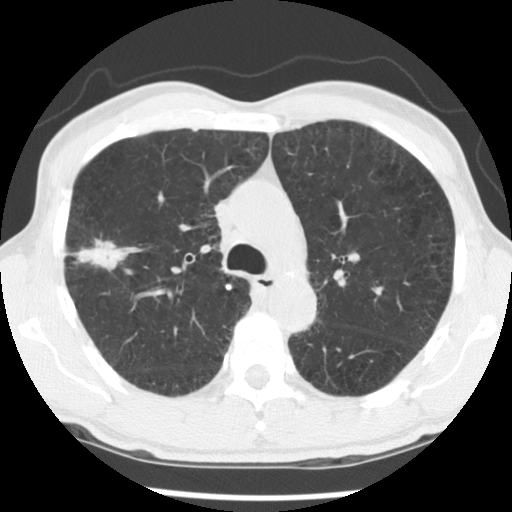
Chest CT (low-dose screening protocol), one axial image; second screening round (one year after baseline); lung window (W 1500 / L -600 HU); standard (soft-tissue) reconstruction kernel (STANDARD); 140 kVp; 512 × 512 image matrix, field of view 320 × 320 mm. Male participant, aged 56 years at enrolment. Current smoker at enrolment.
Lesion marked by an expert reader, box from (x=53, y=231) to (x=139, y=293) px. Reader record for this screening exam (exam-level; its link to the box is not recorded): non-calcified nodule or mass ≥4 mm, right upper lobe, 30 × 18 mm, spiculated (stellate) margins, mixed attenuation, pre-existing on the prior screen: yes; interval growth: yes. Official screen result: positive, other. Participant outcome: lung cancer diagnosed 326 days after this screen — squamous cell carcinoma, NOS, right upper lobe, right middle lobe, moderately differentiated (G2), stage IB (AJCC 6th edition), 70 mm at pathology.